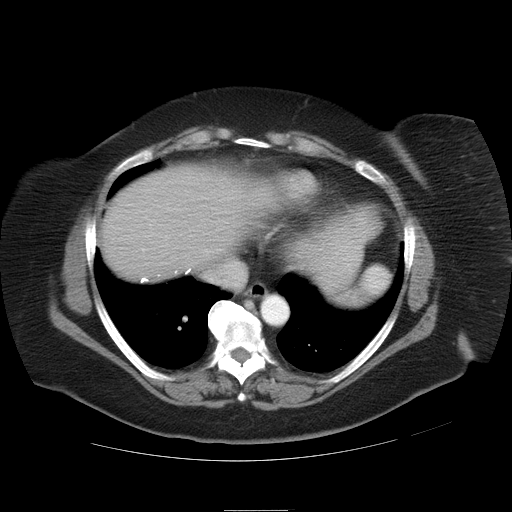
Contrast-enhanced abdominal CT, one axial slice. Slice 33 of 37 in the series (ordered by position). Reconstruction kernel STANDARD. Intravenous contrast given. Soft-tissue window (W 400 / L 40 HU). 7.5 mm slice thickness. 512 × 512 image matrix. Female patient, age 68 years. From the clinical record (not read from this slice): diagnosis: colorectal cancer liver metastases, imaged before liver resection; multiple liver metastases: no; largest metastasis: 2 cm.
Annotated regions visible in this slice (manually delineated by an expert):
- liver: bounding box [x1, y1, x2, y2] px = [101, 163, 286, 283]
- planned liver remnant (the part of the liver to remain after resection): [101, 163, 285, 283]